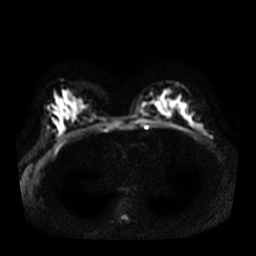
Breast MRI, one axial slice; position 17 of 30 along the scan axis; diffusion-weighted series; image 2 of 4 stored at this slice position (different b-values; order by instance number); 3 T; 256 × 256 image matrix, field of view 340 × 340 mm. Female patient.
Outlined on this slice (outlined manually by an expert reader):
- tumour on diffusion-weighted imaging: box from (x=205, y=135) to (x=210, y=137) px